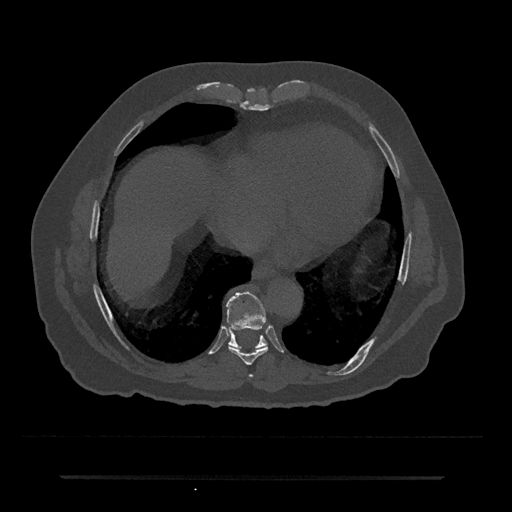
CT including the spine, one axial slice; position 310 of 797 along the scan axis; reconstruction kernel Br40s/3; 120 kVp; bone window (W 1800 / L 400 HU); 512 × 512 image matrix, field of view 437 × 437 mm. Patient: male, 69 years. From the clinical record (not read from this slice): primary cancer: prostate.
Annotated regions visible in this slice (semi-automatically segmented with operator editing):
- T7 vertebra: bounding box <249,375,253,378> (left, top, right, bottom; pixels)
- T8 vertebra: <228,345,268,365>
- T9 vertebra: <226,291,267,348>